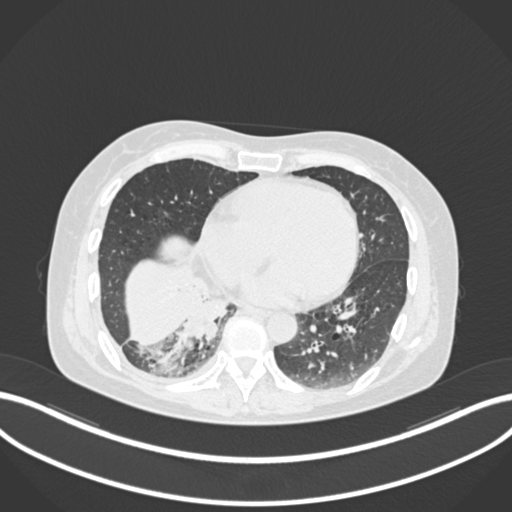
Chest CT, one axial slice. Slice 53 of 168 in the series (ordered by position). Reconstruction kernel B30f. 120 kVp. Lung window (W 1500 / L -600 HU). 1 mm slice thickness. 512 × 512 image matrix, field of view 400 × 400 mm. Female patient, age 63 years. Case-level facts recorded for this patient, not image findings: clinical TNM (as recorded): T1c N0 M0.
Outlined on this slice (rectangle marked by the reading radiologist):
- lung tumour (recorded histology: adenocarcinoma): bounding box (x1, y1, x2, y2) in pixels: (183, 286, 233, 346)